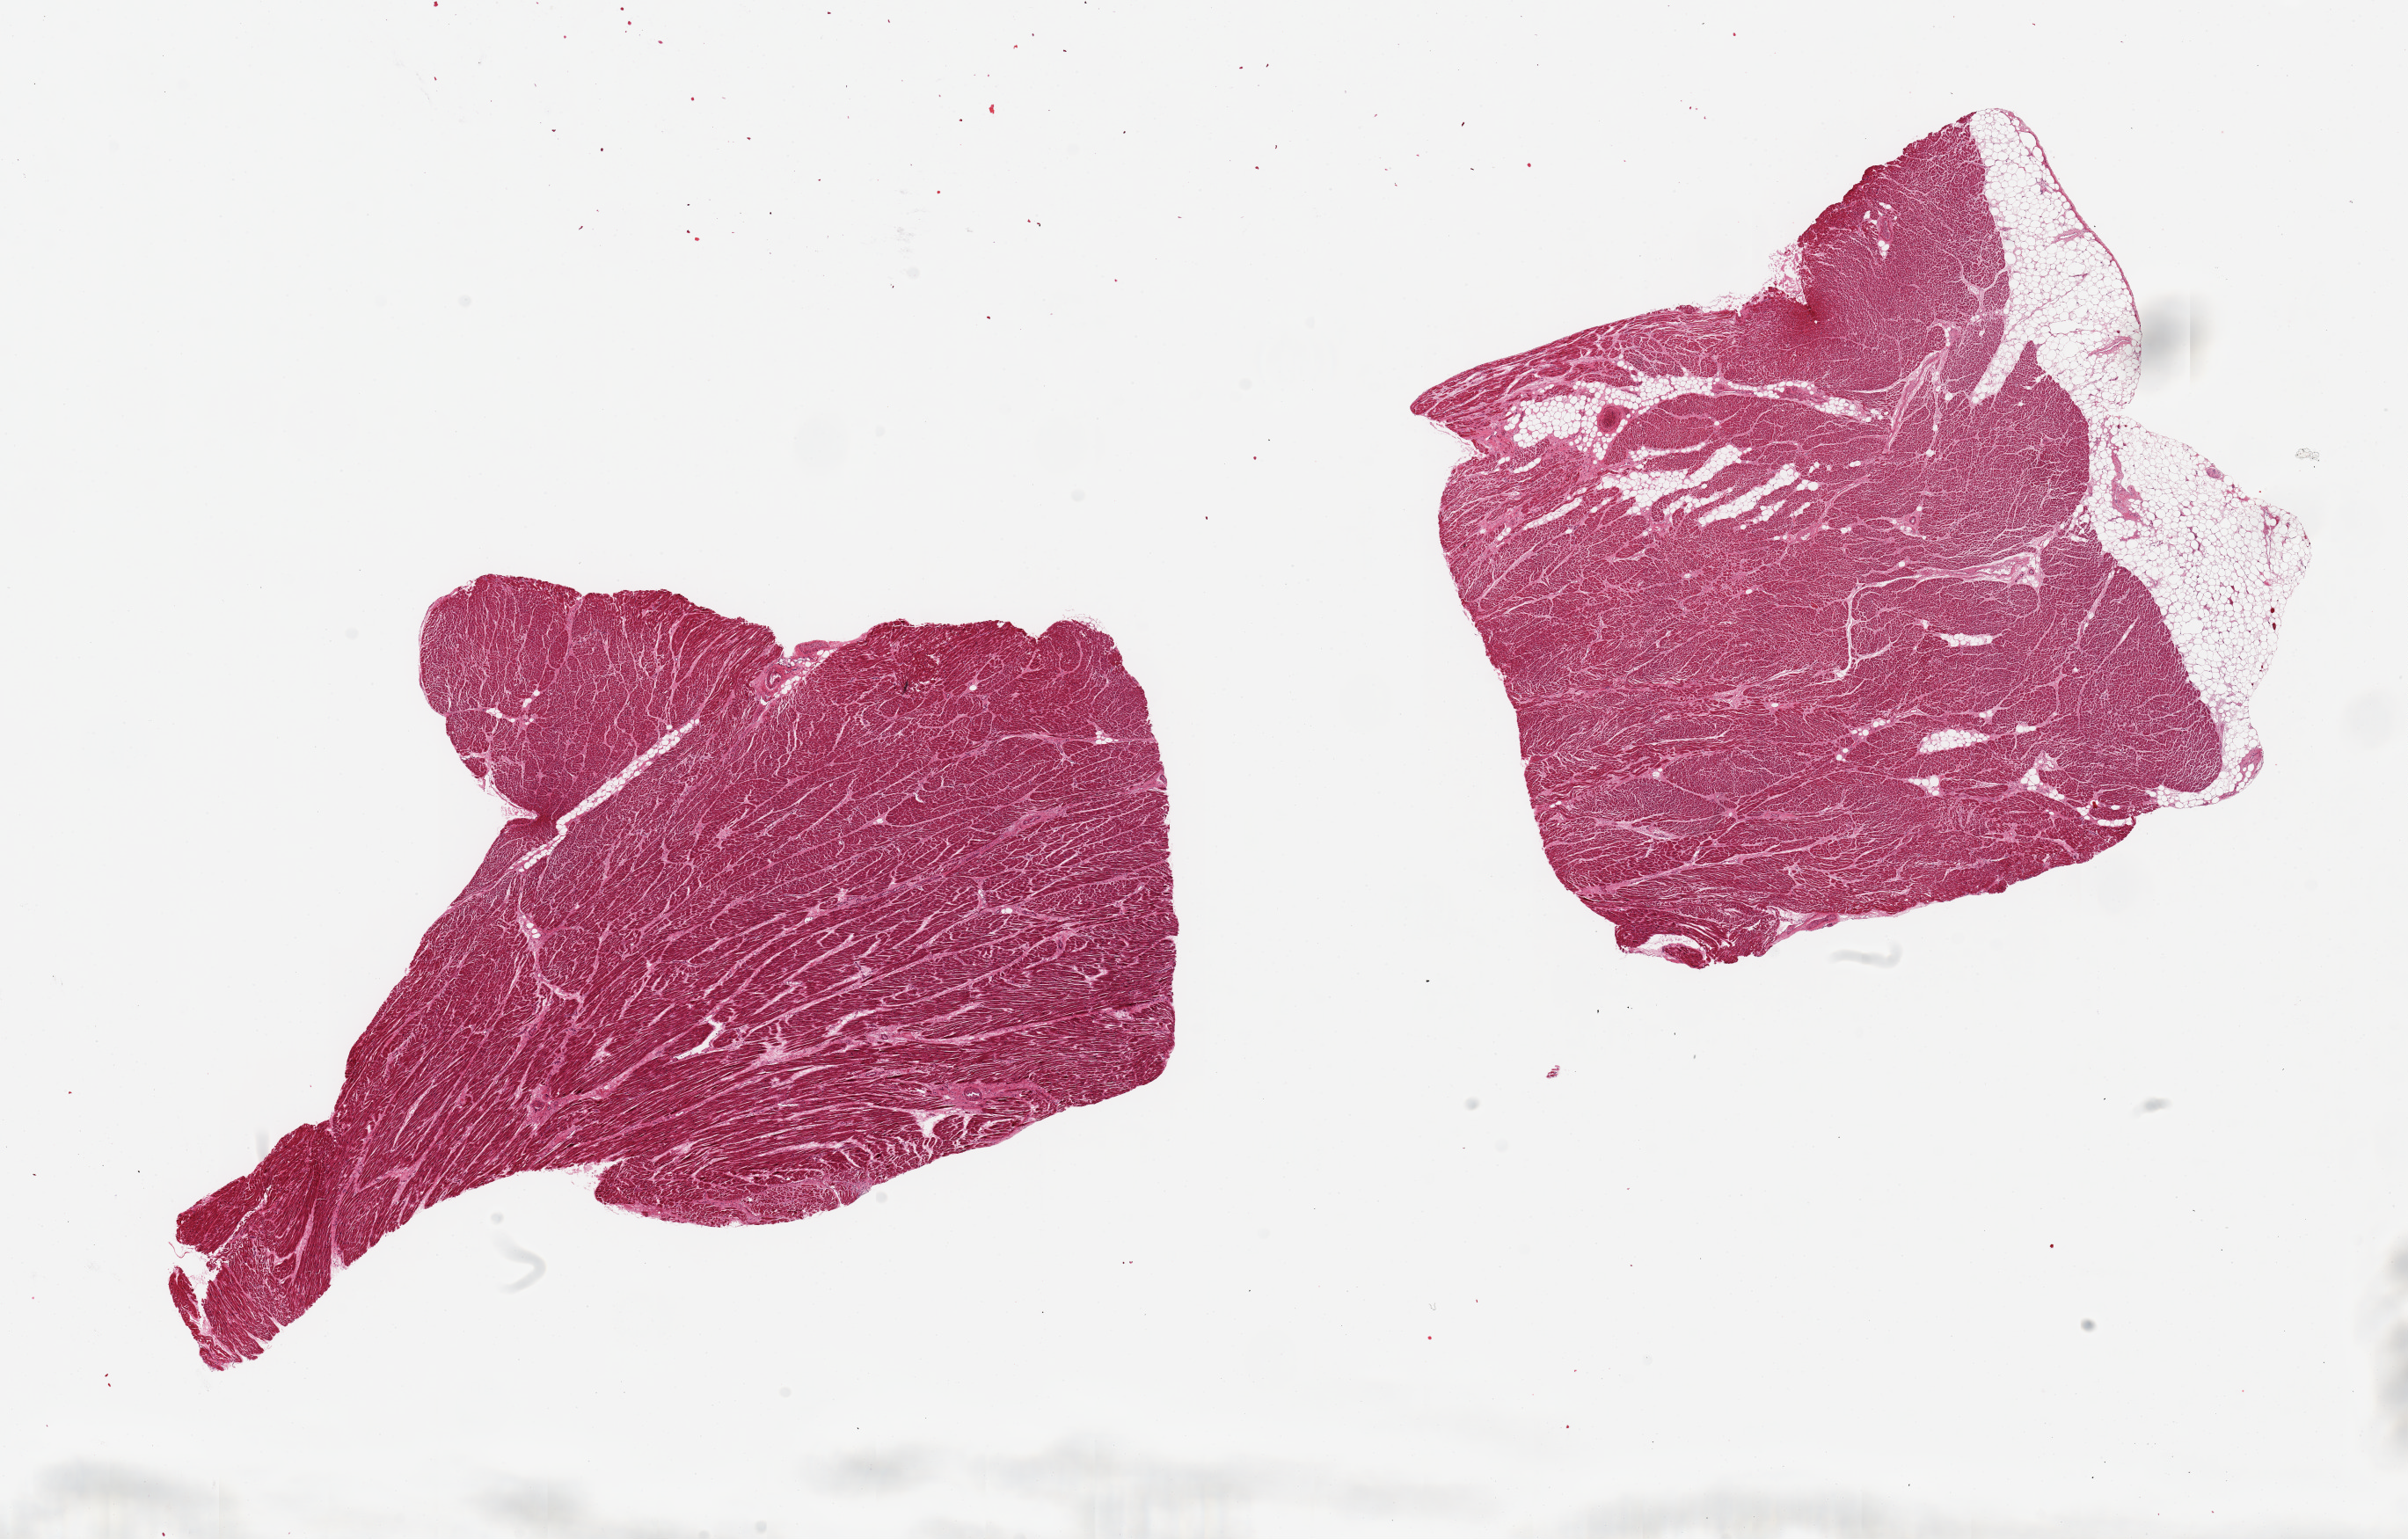
H&E whole-slide image, low-resolution overview of the scanned area, about 21.7 x 13.8 mm (from a 20x scan), PAXgene-fixed paraffin-embedded (PFPE) section, section of heart (target tissue), donor tissue sample. Female donor.
Pathologist's review note for this sample: 2 pieces~8x5mm, minimal ischemic changes; One aliquot ~5-10% fat, one edge.